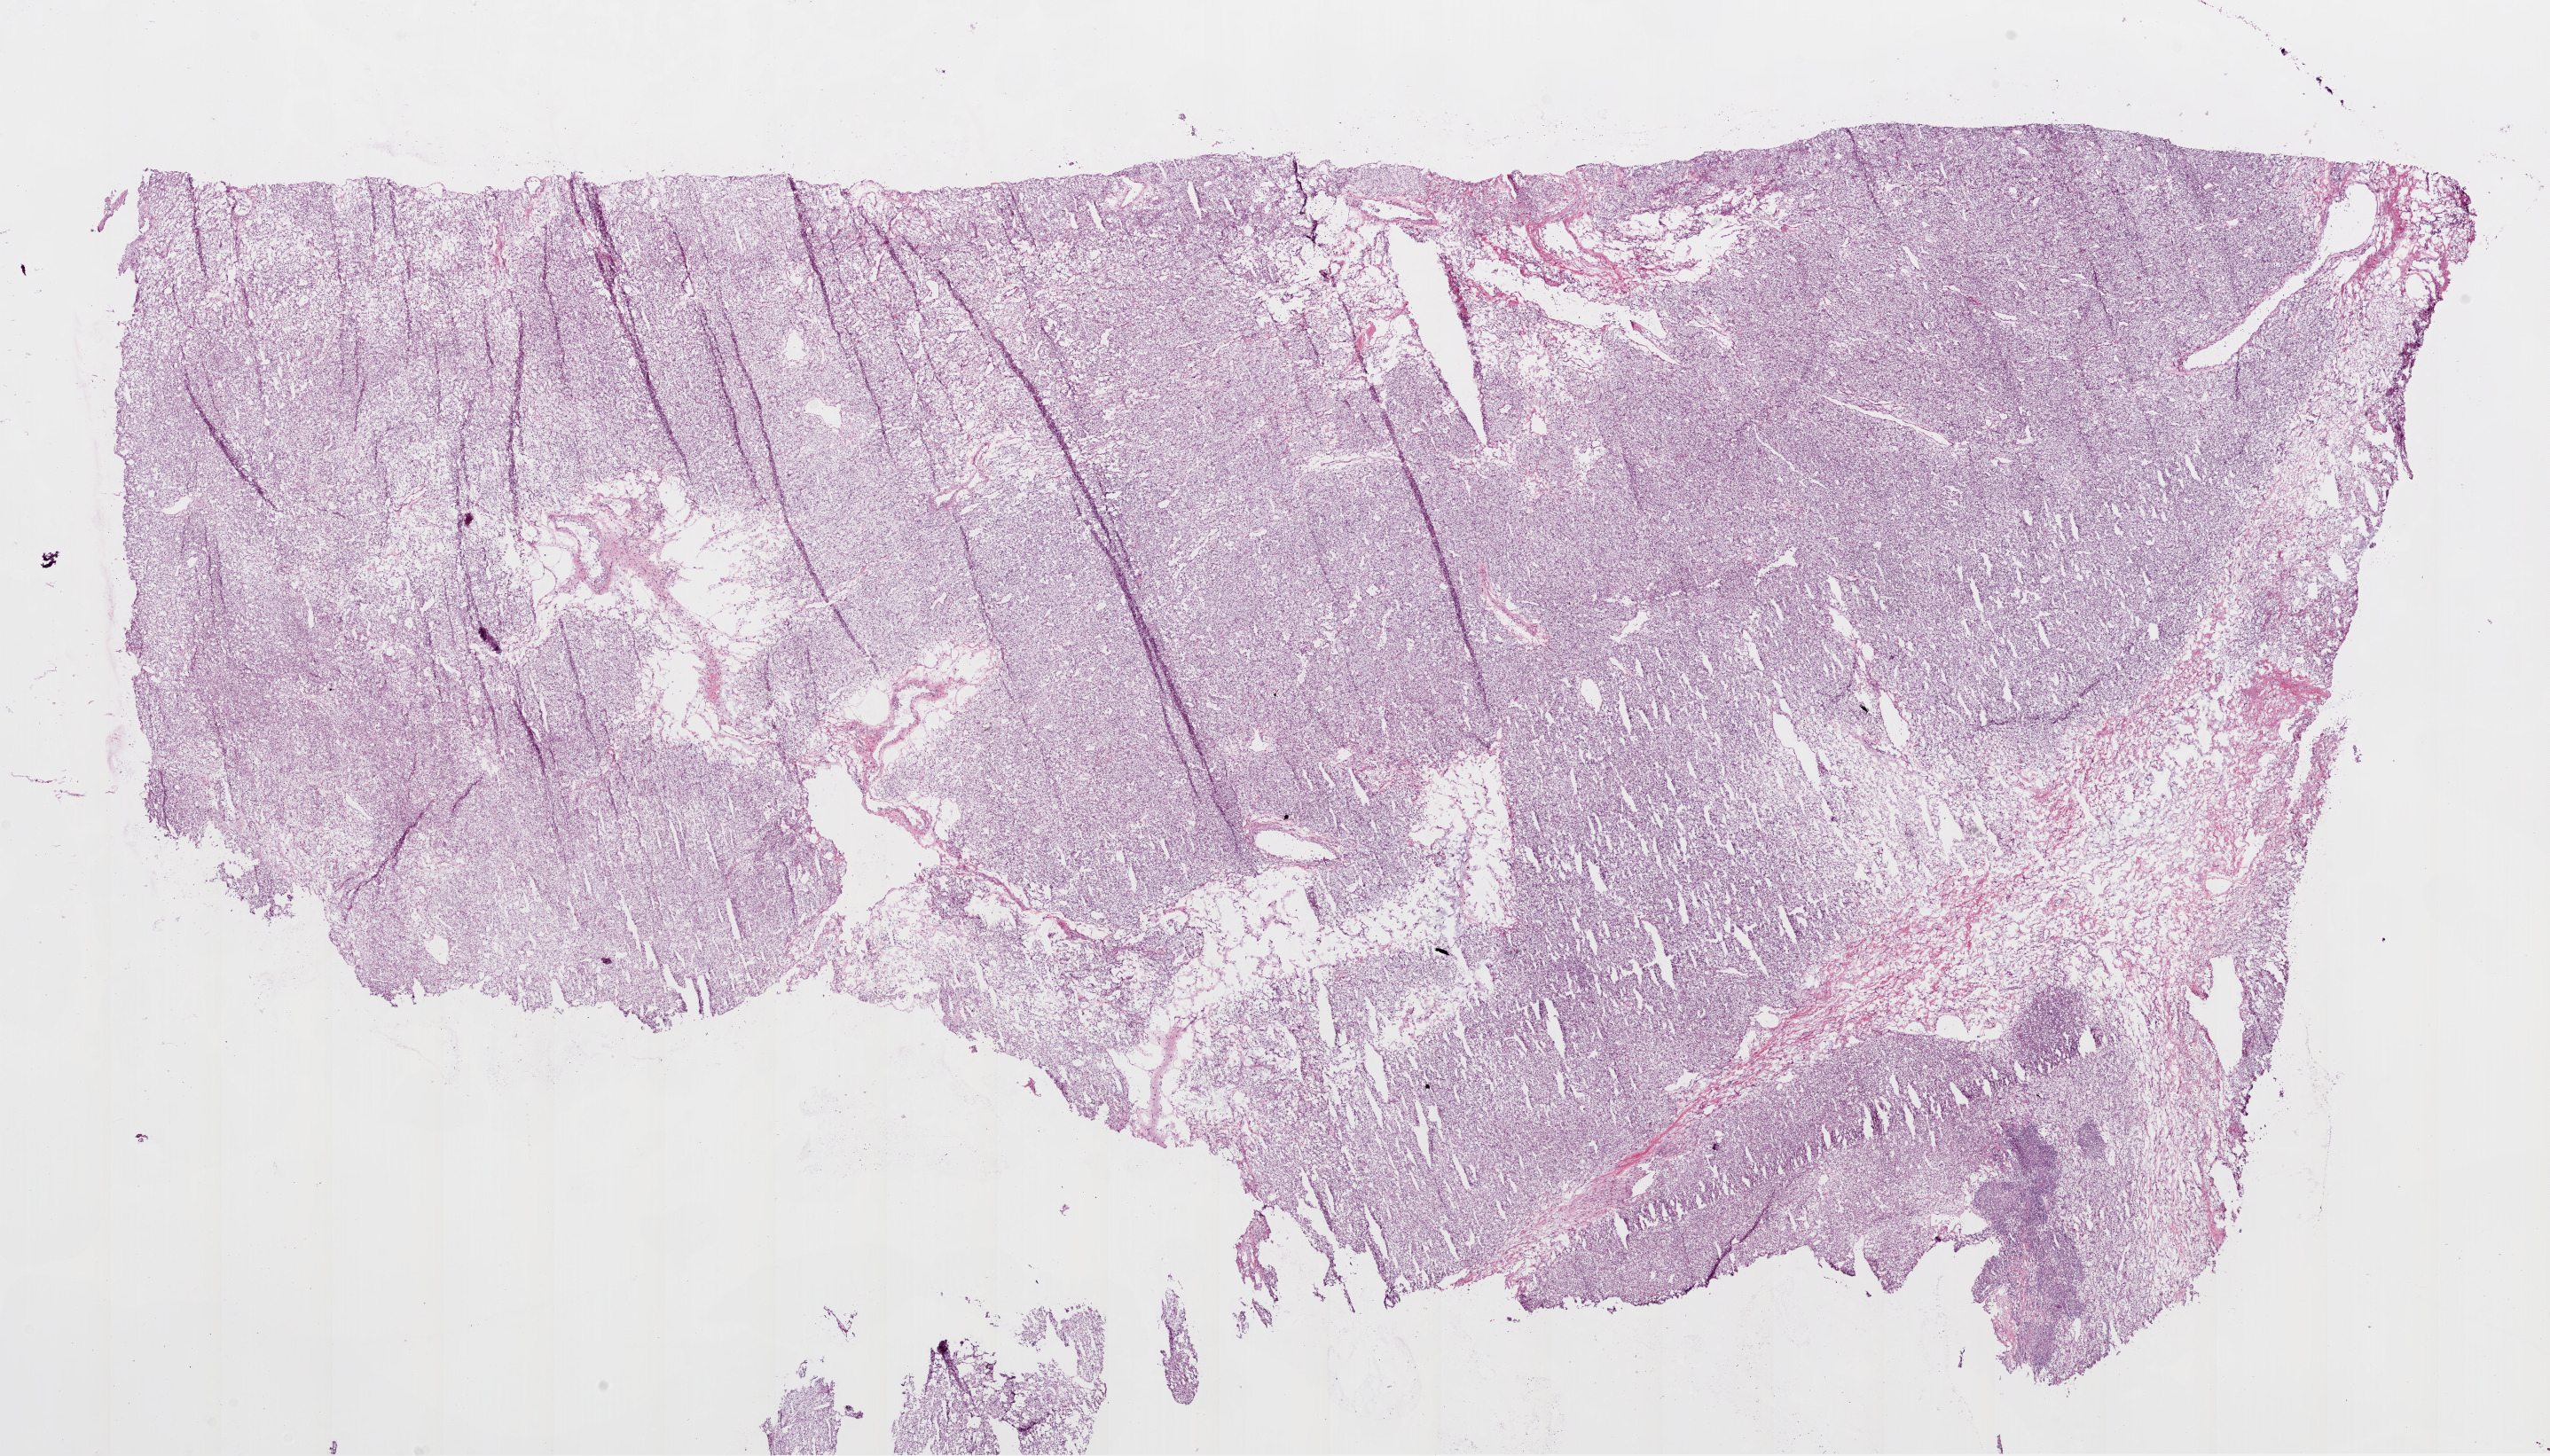
Digitized H&E-stained tissue section (whole slide) — a low-resolution overview of the entire scanned area, about 23.1 x 13.2 mm (acquisition: 20x scan), frozen section, primary tumour sample from the kidney. Patient: male, age at initial diagnosis 50 years. Histologic grade: G3 (poorly differentiated). Composition of this section per pathologist review: tumour cells 85%, tumour nuclei 85%, normal cells 0%, stromal cells 15%, necrosis 0%.
Diagnosis: Clear cell adenocarcinoma, NOS. AJCC pathologic stage: III (6th edition).